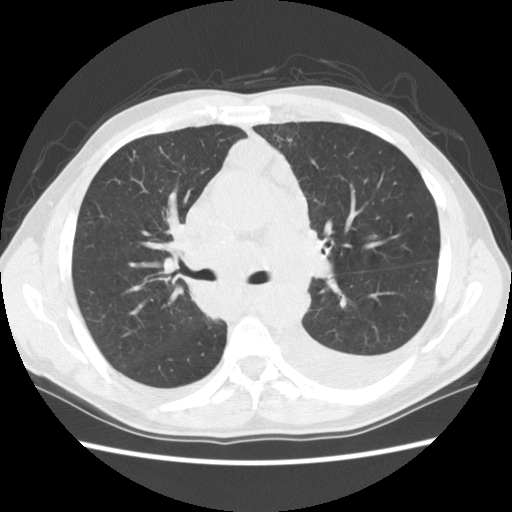
Chest CT (low-dose screening protocol), one axial image; baseline annual screen; lung window (W 1500 / L -600 HU); 2.5 mm slice thickness; standard (soft-tissue) reconstruction kernel (STANDARD); 512 × 512 image matrix, field of view 346 × 346 mm. Male participant, aged 60 years at enrolment. Current smoker at enrolment.
• Lesion marked by an expert reader, bounding box (x1, y1, x2, y2) in pixels: (178, 236, 293, 326).
• No non-calcified nodule or mass ≥4 mm was recorded by the screening reader at this exam.
• Participant outcome: lung cancer diagnosed 12 days after this screen — squamous cell carcinoma, NOS, carina, poorly differentiated (G3), stage IV (AJCC 6th edition).